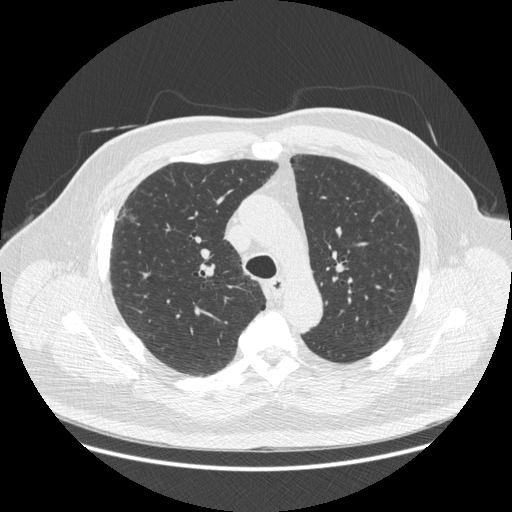
Chest CT (low-dose screening protocol), one axial image; baseline annual screen; lung window (W 1500 / L -600 HU); 1.25 mm slice thickness; standard (soft-tissue) reconstruction kernel (STANDARD); slice 83 of 266 in the series; 512 × 512 image matrix, field of view 404 × 404 mm. Male participant, aged 66 years at enrolment. Current smoker at enrolment.
Expert-annotated lung lesion, bounding box (x1, y1, x2, y2) in pixels: (110, 204, 146, 232). Screening reader's record for this exam: no non-calcified nodule ≥4 mm recorded. Lung cancer was diagnosed 742 days after this screen: non-small cell carcinoma, right upper lobe, stage IV (AJCC 6th edition), 50 mm at pathology.